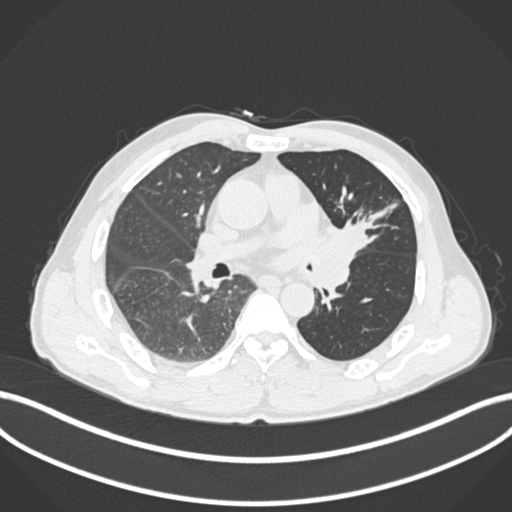
Chest CT, one axial slice; 120 kVp; lung window (W 1500 / L -600 HU); 512 × 512 image matrix, field of view 400 × 400 mm. Male patient, age 57 years. From the clinical record (not read from this slice): clinical TNM (as recorded): T2b N0 M0.
Structures marked on this image (rectangle marked by the reading radiologist):
- lung tumour (recorded histology: squamous cell carcinoma): bounding box <321,217,373,264> (left, top, right, bottom; pixels)